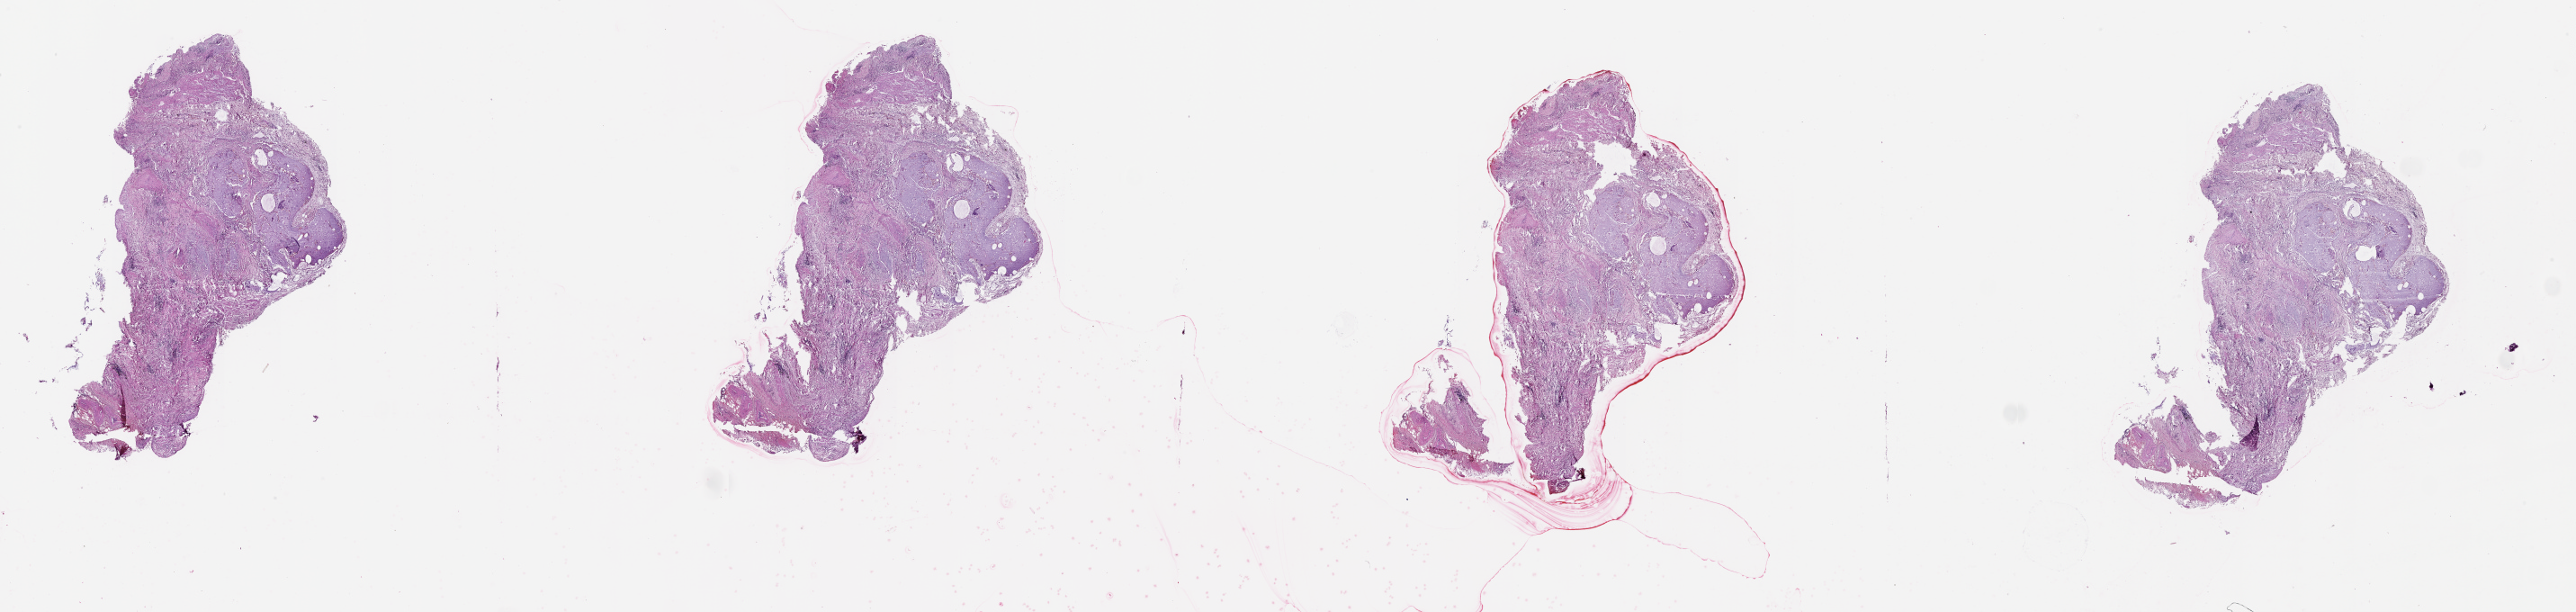
Hematoxylin and eosin (H&E) stained whole-slide image — shown as a low-resolution overview of the whole scanned area (about 46.1 x 10.9 mm, from a 20x scan). Lung, normal (non-tumour) tissue. Patient: male, age 72 years.
• this section: normal (non-tumour) tissue from the same patient
• patient diagnosis (cohort enrolment): squamous cell carcinoma (lung)